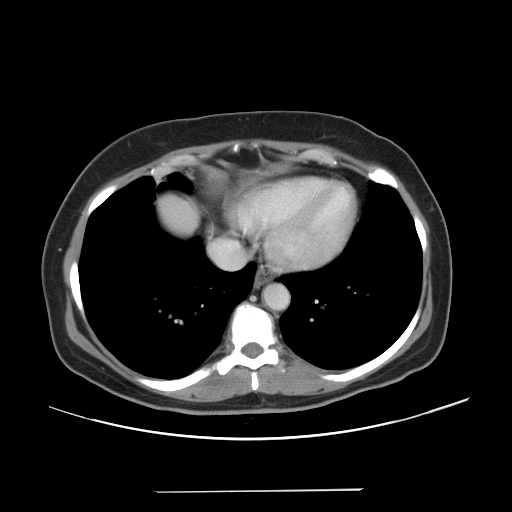
Contrast-enhanced abdominal CT, one axial slice. Slice 45 of 56 in the series (ordered by position). 120 kVp. Intravenous contrast given. Soft-tissue window (W 400 / L 40 HU). 5 mm slice thickness. 512 × 512 image matrix, field of view 419 × 419 mm. Female patient, age 54 years. Case-level facts recorded for this patient, not image findings: diagnosis: colorectal cancer liver metastases, imaged before liver resection; multiple liver metastases: yes; largest metastasis: 3.2 cm.
Structures marked on this image (expert manual segmentation):
- liver: bounding box <159,198,197,235> (left, top, right, bottom; pixels)